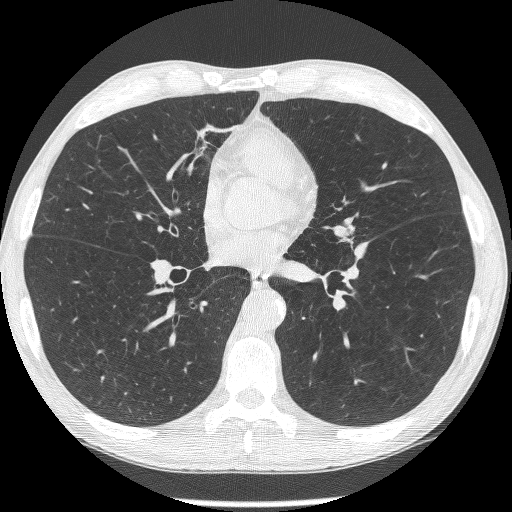
Chest CT (low-dose screening protocol), one axial image, second annual screen, lung window (W 1500 / L -600 HU), 1.25 mm slice thickness, 120 kVp. Male, age 62 years at enrolment. Former smoker at enrolment.
• Expert reader's lesion annotation, box from (x=322, y=216) to (x=370, y=264) px.
• The screening reader recorded 2 non-calcified nodules or masses ≥4 mm on this exam (lingula, lingula); which of them this box marks is not recorded.
• Official screen result: positive, other.